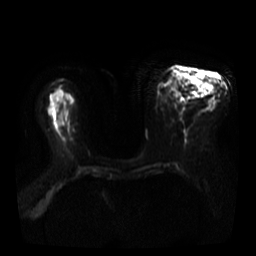
Breast MRI, one axial slice. Slice 18 of 40 in the series (ordered by position). Diffusion-weighted series; image 2 of 4 stored at this slice position (different b-values; order by instance number). 3 T. 5 mm slice thickness. 256 × 256 image matrix, field of view 360 × 360 mm. Female patient.
Outlined on this slice (manually delineated by an expert):
- tumour on diffusion-weighted imaging: bounding box <190,75,202,86> (left, top, right, bottom; pixels)